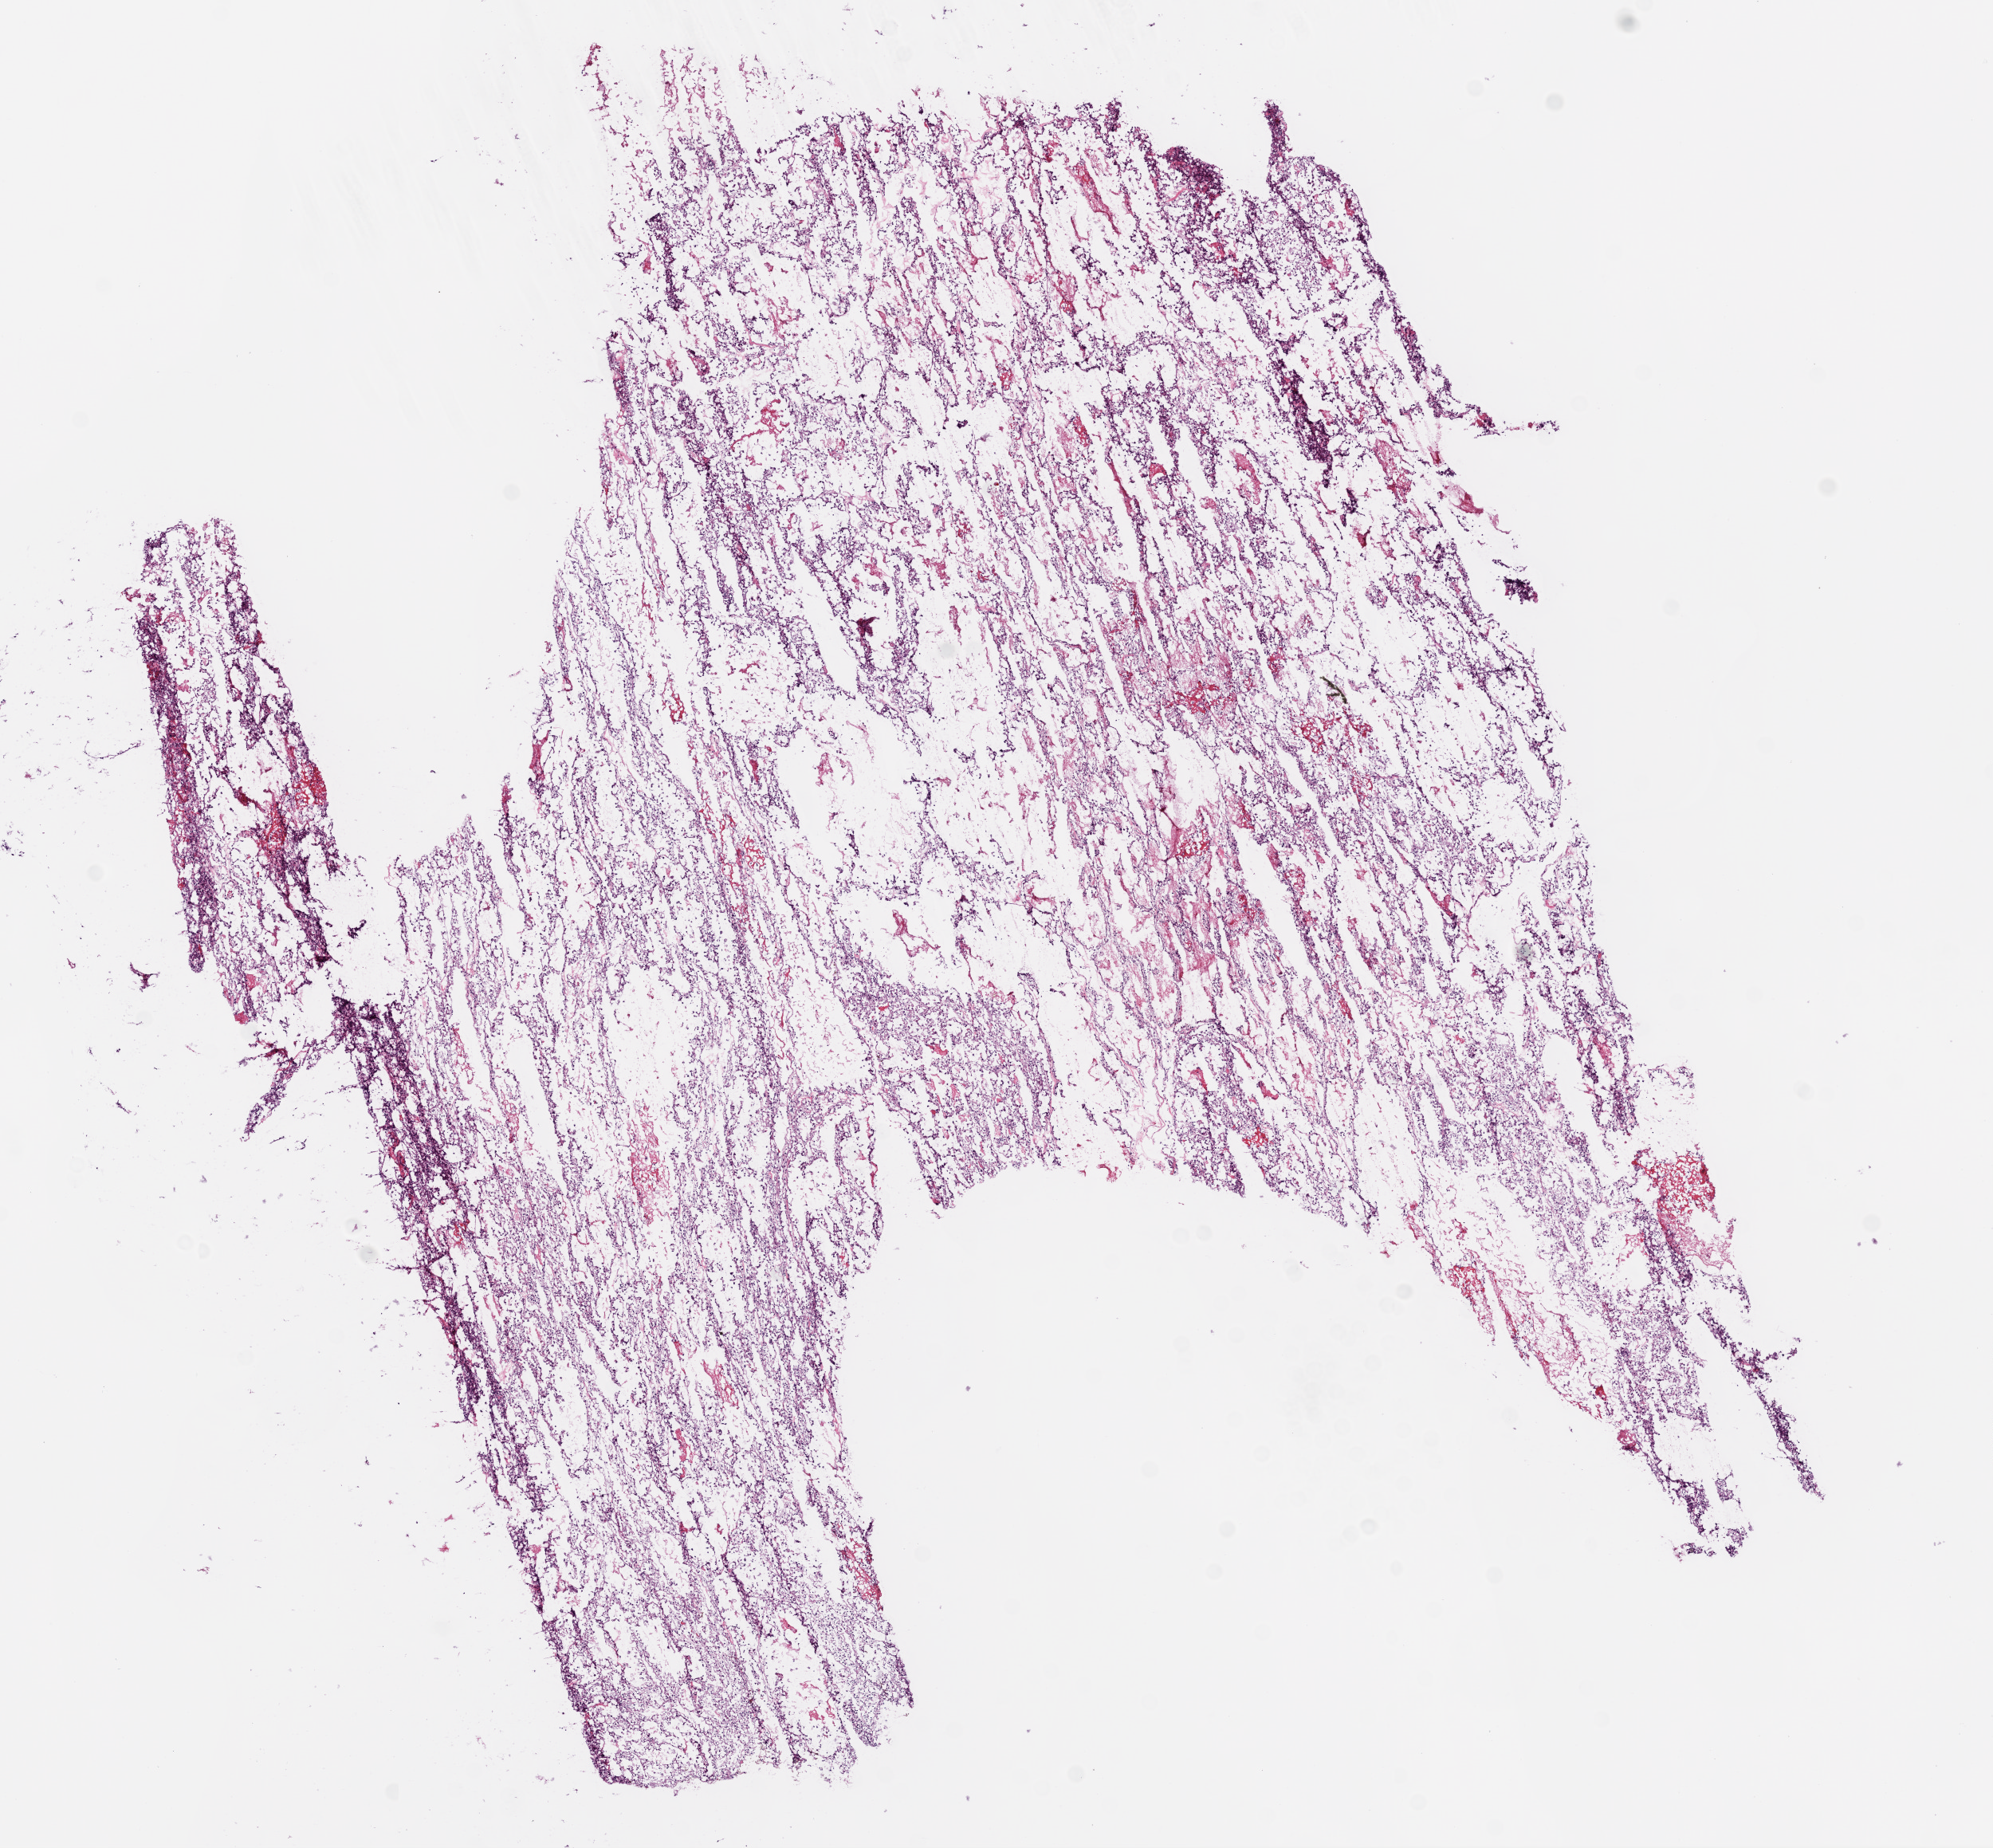
Whole-slide histology image, H&E, low-resolution overview of the scanned area, about 10.0 x 9.3 mm (from a 20x scan). Frozen section. Primary tumour sample from the kidney. Patient: male, age at initial diagnosis 62 years. Histologic grade: G3 (poorly differentiated). Composition of this section per pathologist review: tumour cells 95%, tumour nuclei 80%, normal cells 0%, stromal cells 5%, necrosis 0%.
- AJCC pathologic stage: II
- pathologic diagnosis: Clear cell adenocarcinoma, NOS
- laterality: right
- TNM: T2 N0 M0